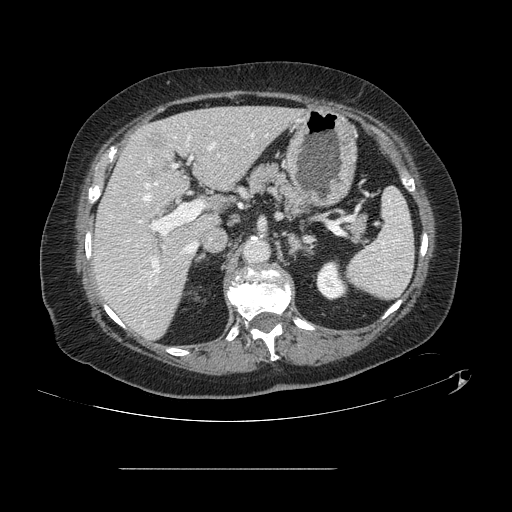
Contrast-enhanced abdominal CT, one axial slice; slice 75 of 148 in the series (ordered by position); intravenous contrast given; soft-tissue window (W 400 / L 40 HU); 2.5 mm slice thickness; 512 × 512 image matrix, field of view 439 × 439 mm. Female patient, age 75 years. From the clinical record (not read from this slice): diagnosis: colorectal cancer liver metastases, imaged before liver resection; multiple liver metastases: no; largest metastasis: 2.4 cm.
Outlined on this slice (manually delineated by an expert):
- hepatic veins: bounding box <144,144,215,252> (left, top, right, bottom; pixels)
- liver: <93,107,298,339>
- planned liver remnant (the part of the liver to remain after resection): <93,107,297,339>
- portal vein (with intrahepatic branches): <138,158,201,274>
- liver metastasis: <149,135,168,146>